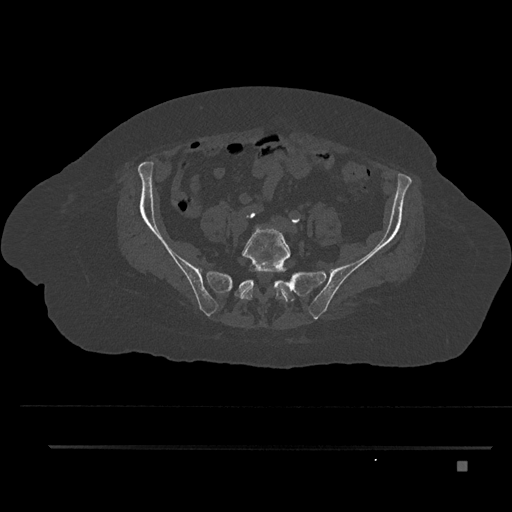
CT including the spine, one axial slice; slice 24 of 797 in the series (ordered by position); reconstruction kernel Br40s/3; 120 kVp; bone window (W 1800 / L 400 HU); 0.5 mm slice thickness; 512 × 512 image matrix. Patient: female, 76 years. Case-level facts recorded for this patient, not image findings: primary cancer: lung; vertebrae with lytic lesions (as recorded): T11, L3.
Outlined on this slice (semi-automatically segmented with operator editing):
- L5 vertebra: bounding box [x1, y1, x2, y2] px = [241, 226, 291, 302]